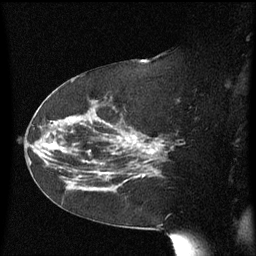
Breast MRI (dynamic contrast-enhanced), one sagittal slice. Slice 34 of 60 in the series (ordered by position). Dynamic contrast-enhanced series, image 2 of 3 at this slice position (ordered by acquisition). 1.5 T. TE 4.2 ms, TR 8.4 ms. 256 × 256 image matrix, field of view 200 × 200 mm. Patient: female, 63 years. Case-level facts recorded for this patient, not image findings: setting: breast cancer imaged before/during neoadjuvant chemotherapy; receptor status: HER2-positive.
Annotated regions visible in this slice (semi-automatic segmentation, software-assisted and operator-edited):
- analysis volume of interest (the breast-tissue region the enhancement analysis was run in; not a lesion): box from (x=63, y=144) to (x=147, y=202) px
- tumour enhancement mask (voxels above the 70 % enhancement threshold inside the analysis volume of interest): (x=98, y=145)–(x=147, y=175)